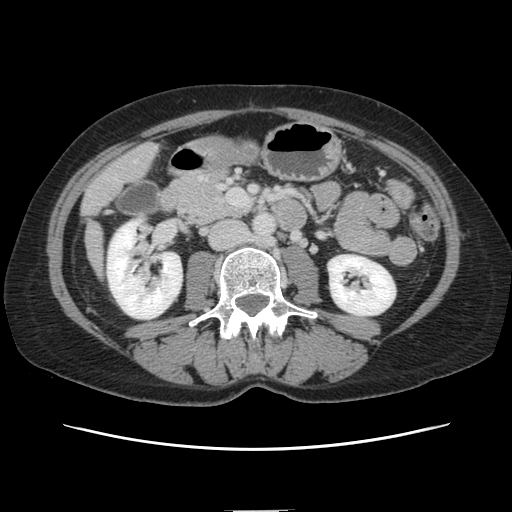
Contrast-enhanced abdominal CT, one axial slice. Position 36 of 141 along the scan axis. Intravenous contrast given. Soft-tissue window (W 400 / L 40 HU). 2.5 mm slice thickness. 512 × 512 image matrix, field of view 350 × 350 mm. Female patient, age 63 years. Case-level facts recorded for this patient, not image findings: diagnosis: colorectal cancer liver metastases, imaged before liver resection; multiple liver metastases: yes.
Outlined on this slice (manually delineated by an expert):
- liver: bounding box [x1, y1, x2, y2] px = [85, 144, 156, 276]